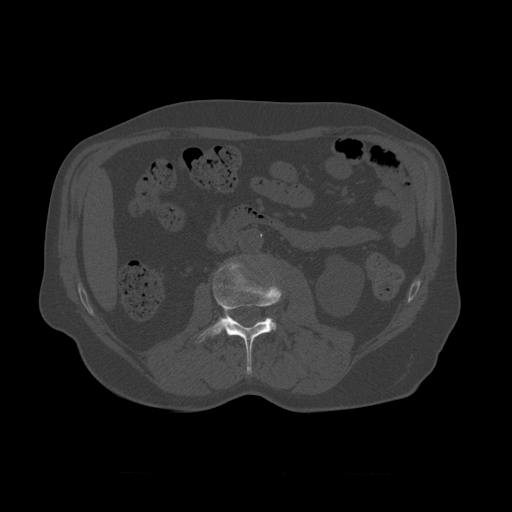
CT including the spine, one axial slice; position 326 of 450 along the scan axis; 120 kVp; bone window (W 1800 / L 400 HU); 512 × 512 image matrix, field of view 405 × 405 mm. Patient age 75 years. Case-level facts recorded for this patient, not image findings: primary cancer: prostate.
Annotated regions visible in this slice (semi-automatically segmented with operator editing):
- L2 vertebra: bounding box <196,261,283,375> (left, top, right, bottom; pixels)
- L3 vertebra: <271,319,277,330>